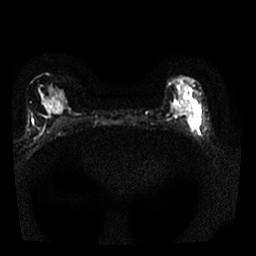
Breast MRI, one axial slice; diffusion-weighted series; image 2 of 4 stored at this slice position (different b-values; order by instance number); 1.5 T; 4 mm slice thickness; 256 × 256 image matrix, field of view 300 × 300 mm. Female patient.
Structures marked on this image (outlined manually by an expert reader):
- tumour on diffusion-weighted imaging: bounding box (x1, y1, x2, y2) in pixels: (197, 116, 201, 125)